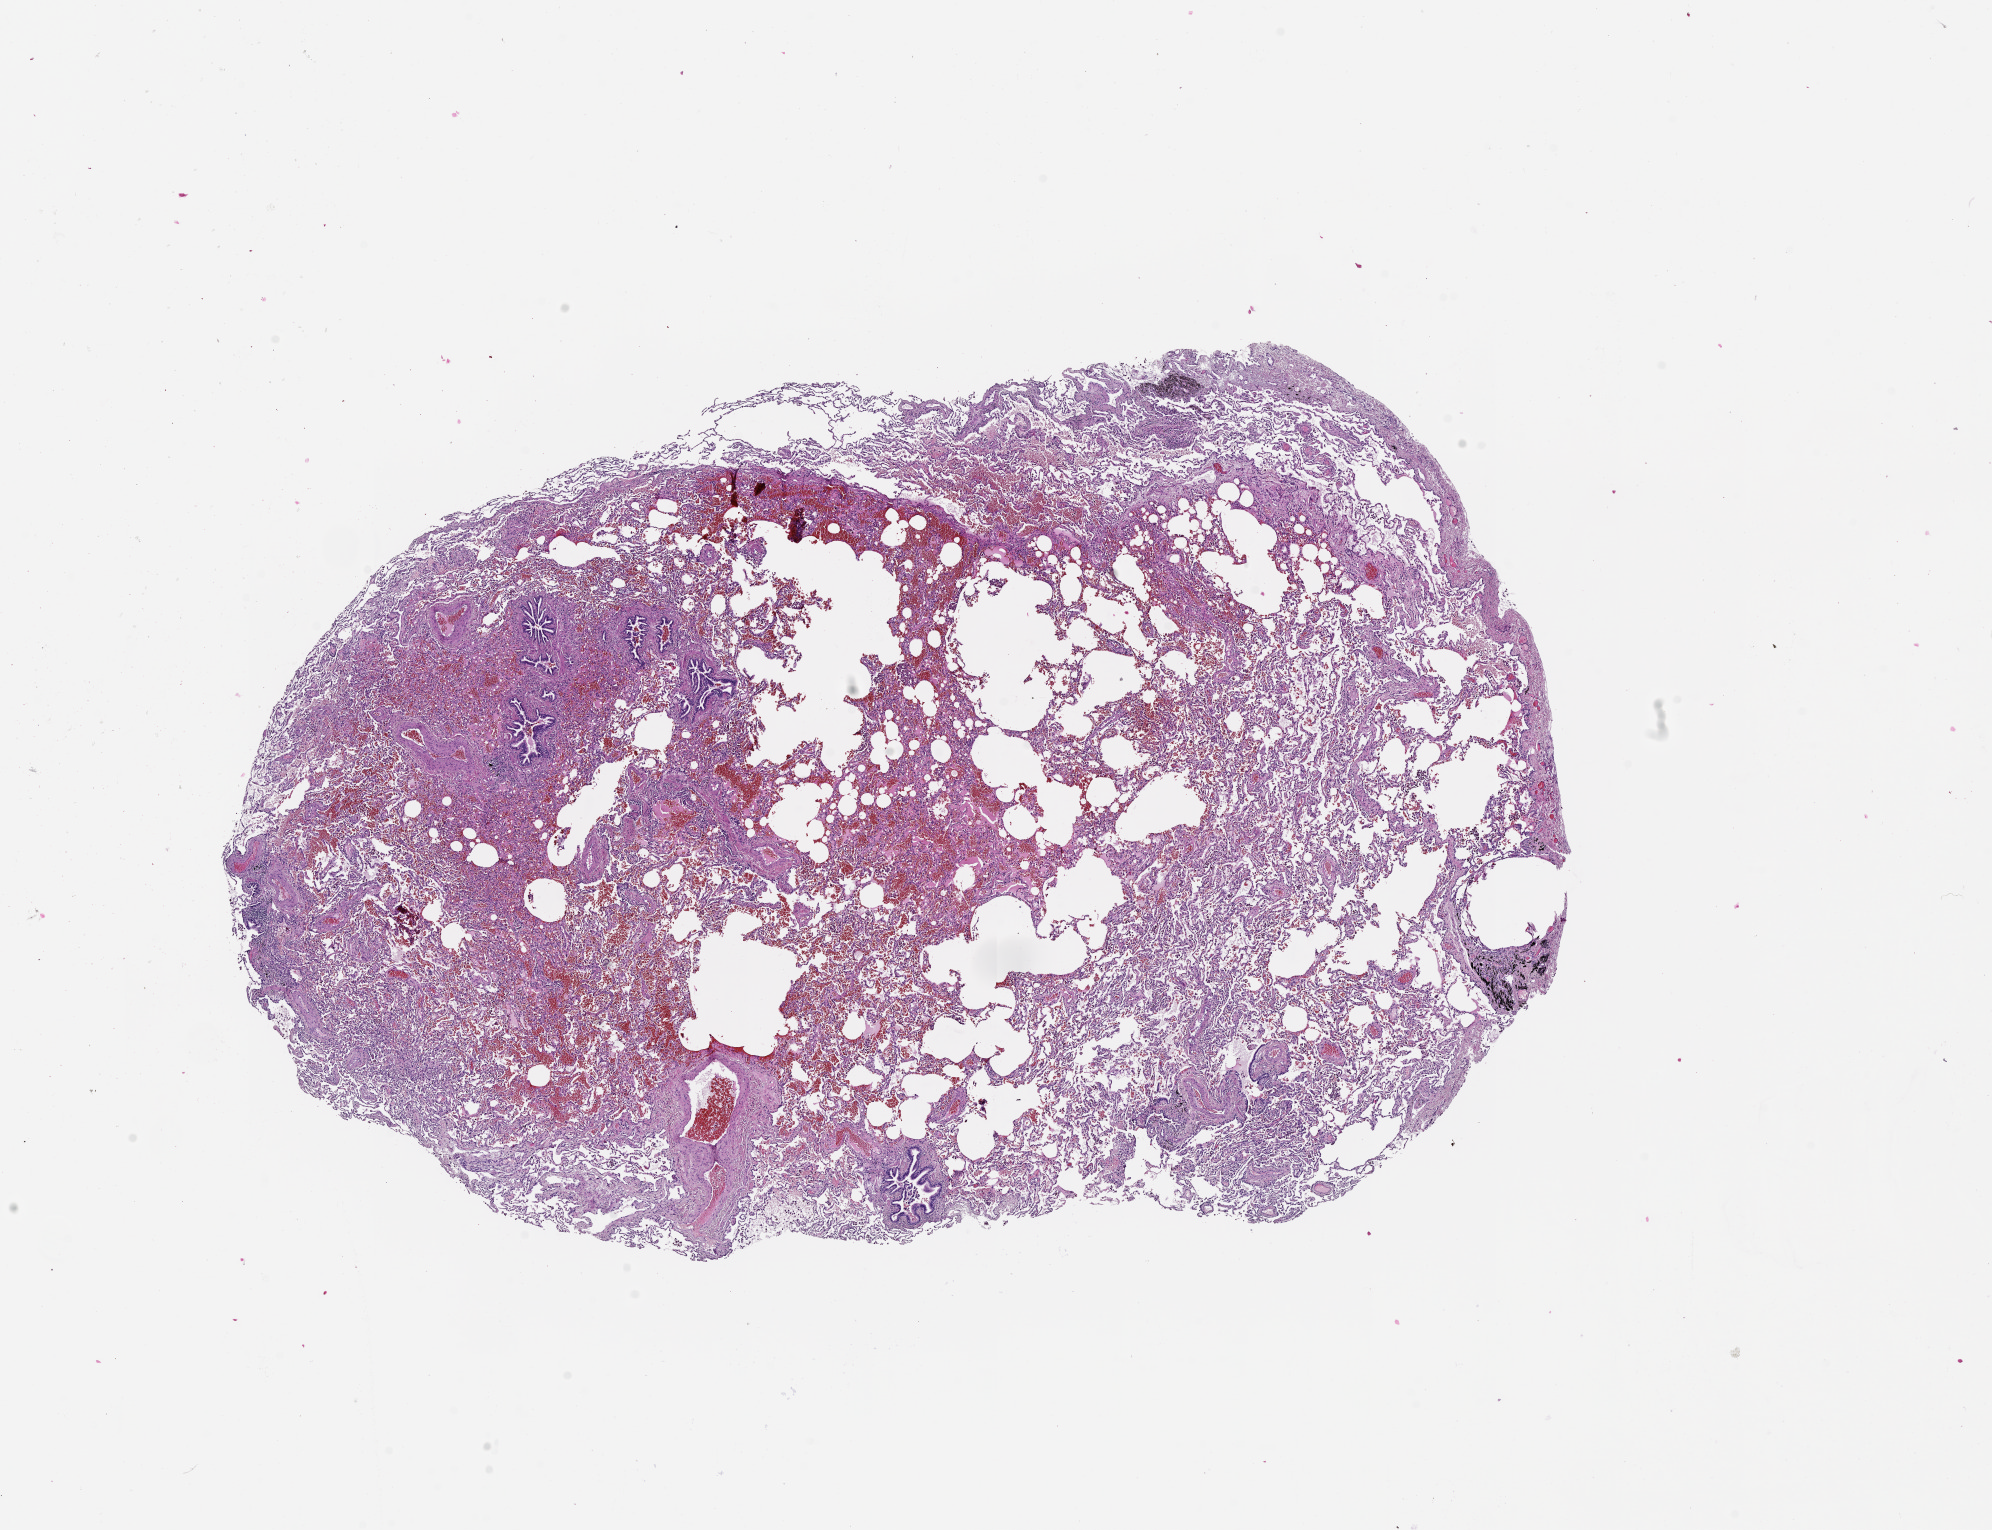
H&E-stained whole-slide image, a low-resolution overview of the entire scanned area, about 16.0 x 12.3 mm (from a 20x scan), normal (non-tumour) tissue sample, lung. Patient: male, age 55 years.
This section: normal (non-tumour) tissue from the same patient. Patient diagnosis (cohort enrolment): squamous cell carcinoma (lung).